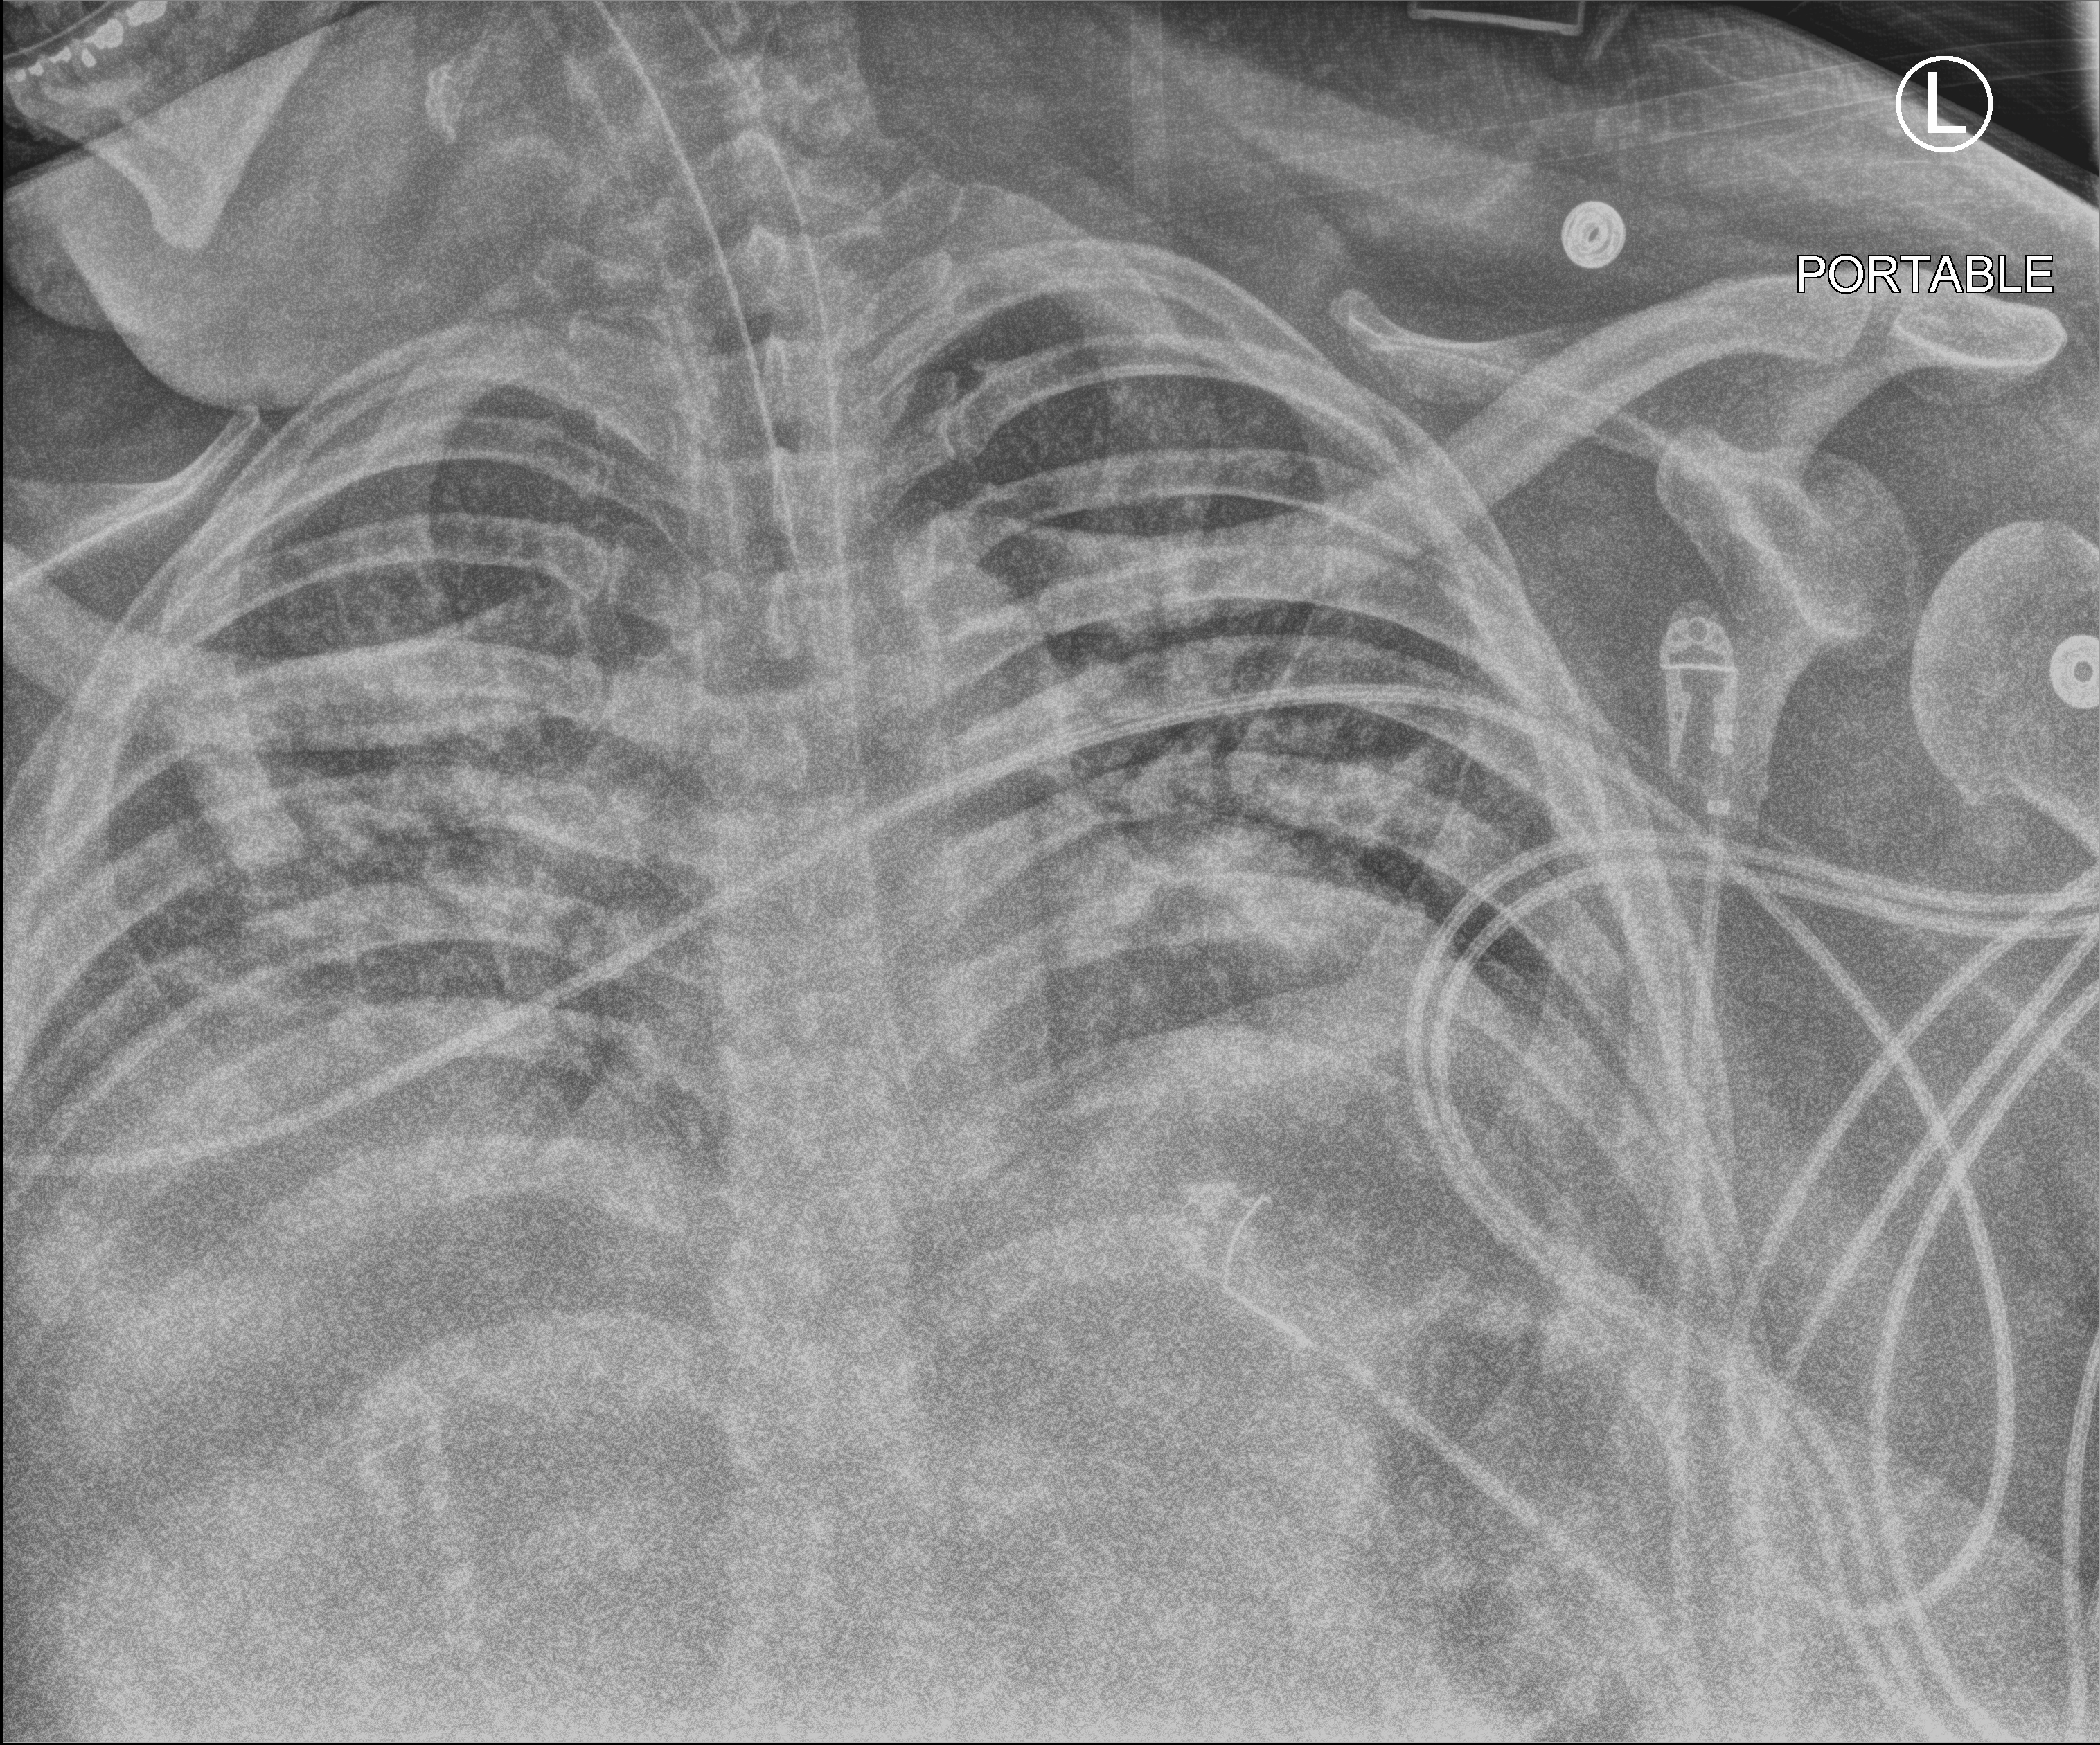
Portable chest radiograph; anteroposterior (AP) projection. Patient hospitalised with COVID-19; male, aged 18–59 years.
From the hospital-stay record, not from the radiograph (when in the stay this image was taken is not recorded): mechanically ventilated during this hospital stay: yes.